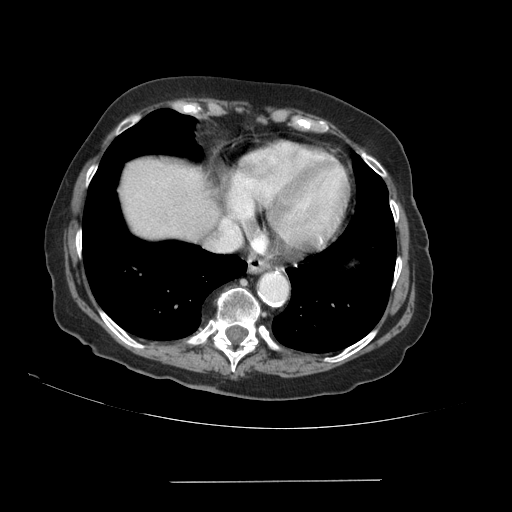
Contrast-enhanced abdominal CT (liver protocol), one axial slice. Position 81 of 89 along the scan axis. 140 kVp. Soft-tissue window (W 400 / L 40 HU). 2.5 mm slice thickness. 512 × 512 image matrix, field of view 400 × 400 mm. Case-level facts recorded for this patient, not image findings: diagnosis: hepatocellular carcinoma (patient treated with transarterial chemoembolisation; whether this scan precedes or follows treatment is not stated here); TNM stage (as recorded): Stage-IVA; Child-Pugh class: A.
Structures marked on this image (semi-automatic segmentation, software-assisted and operator-edited):
- liver parenchyma outside the tumour (the mass and vessels are separate outlines, so this box may not span the whole liver): bounding box [x1, y1, x2, y2] px = [120, 158, 216, 238]